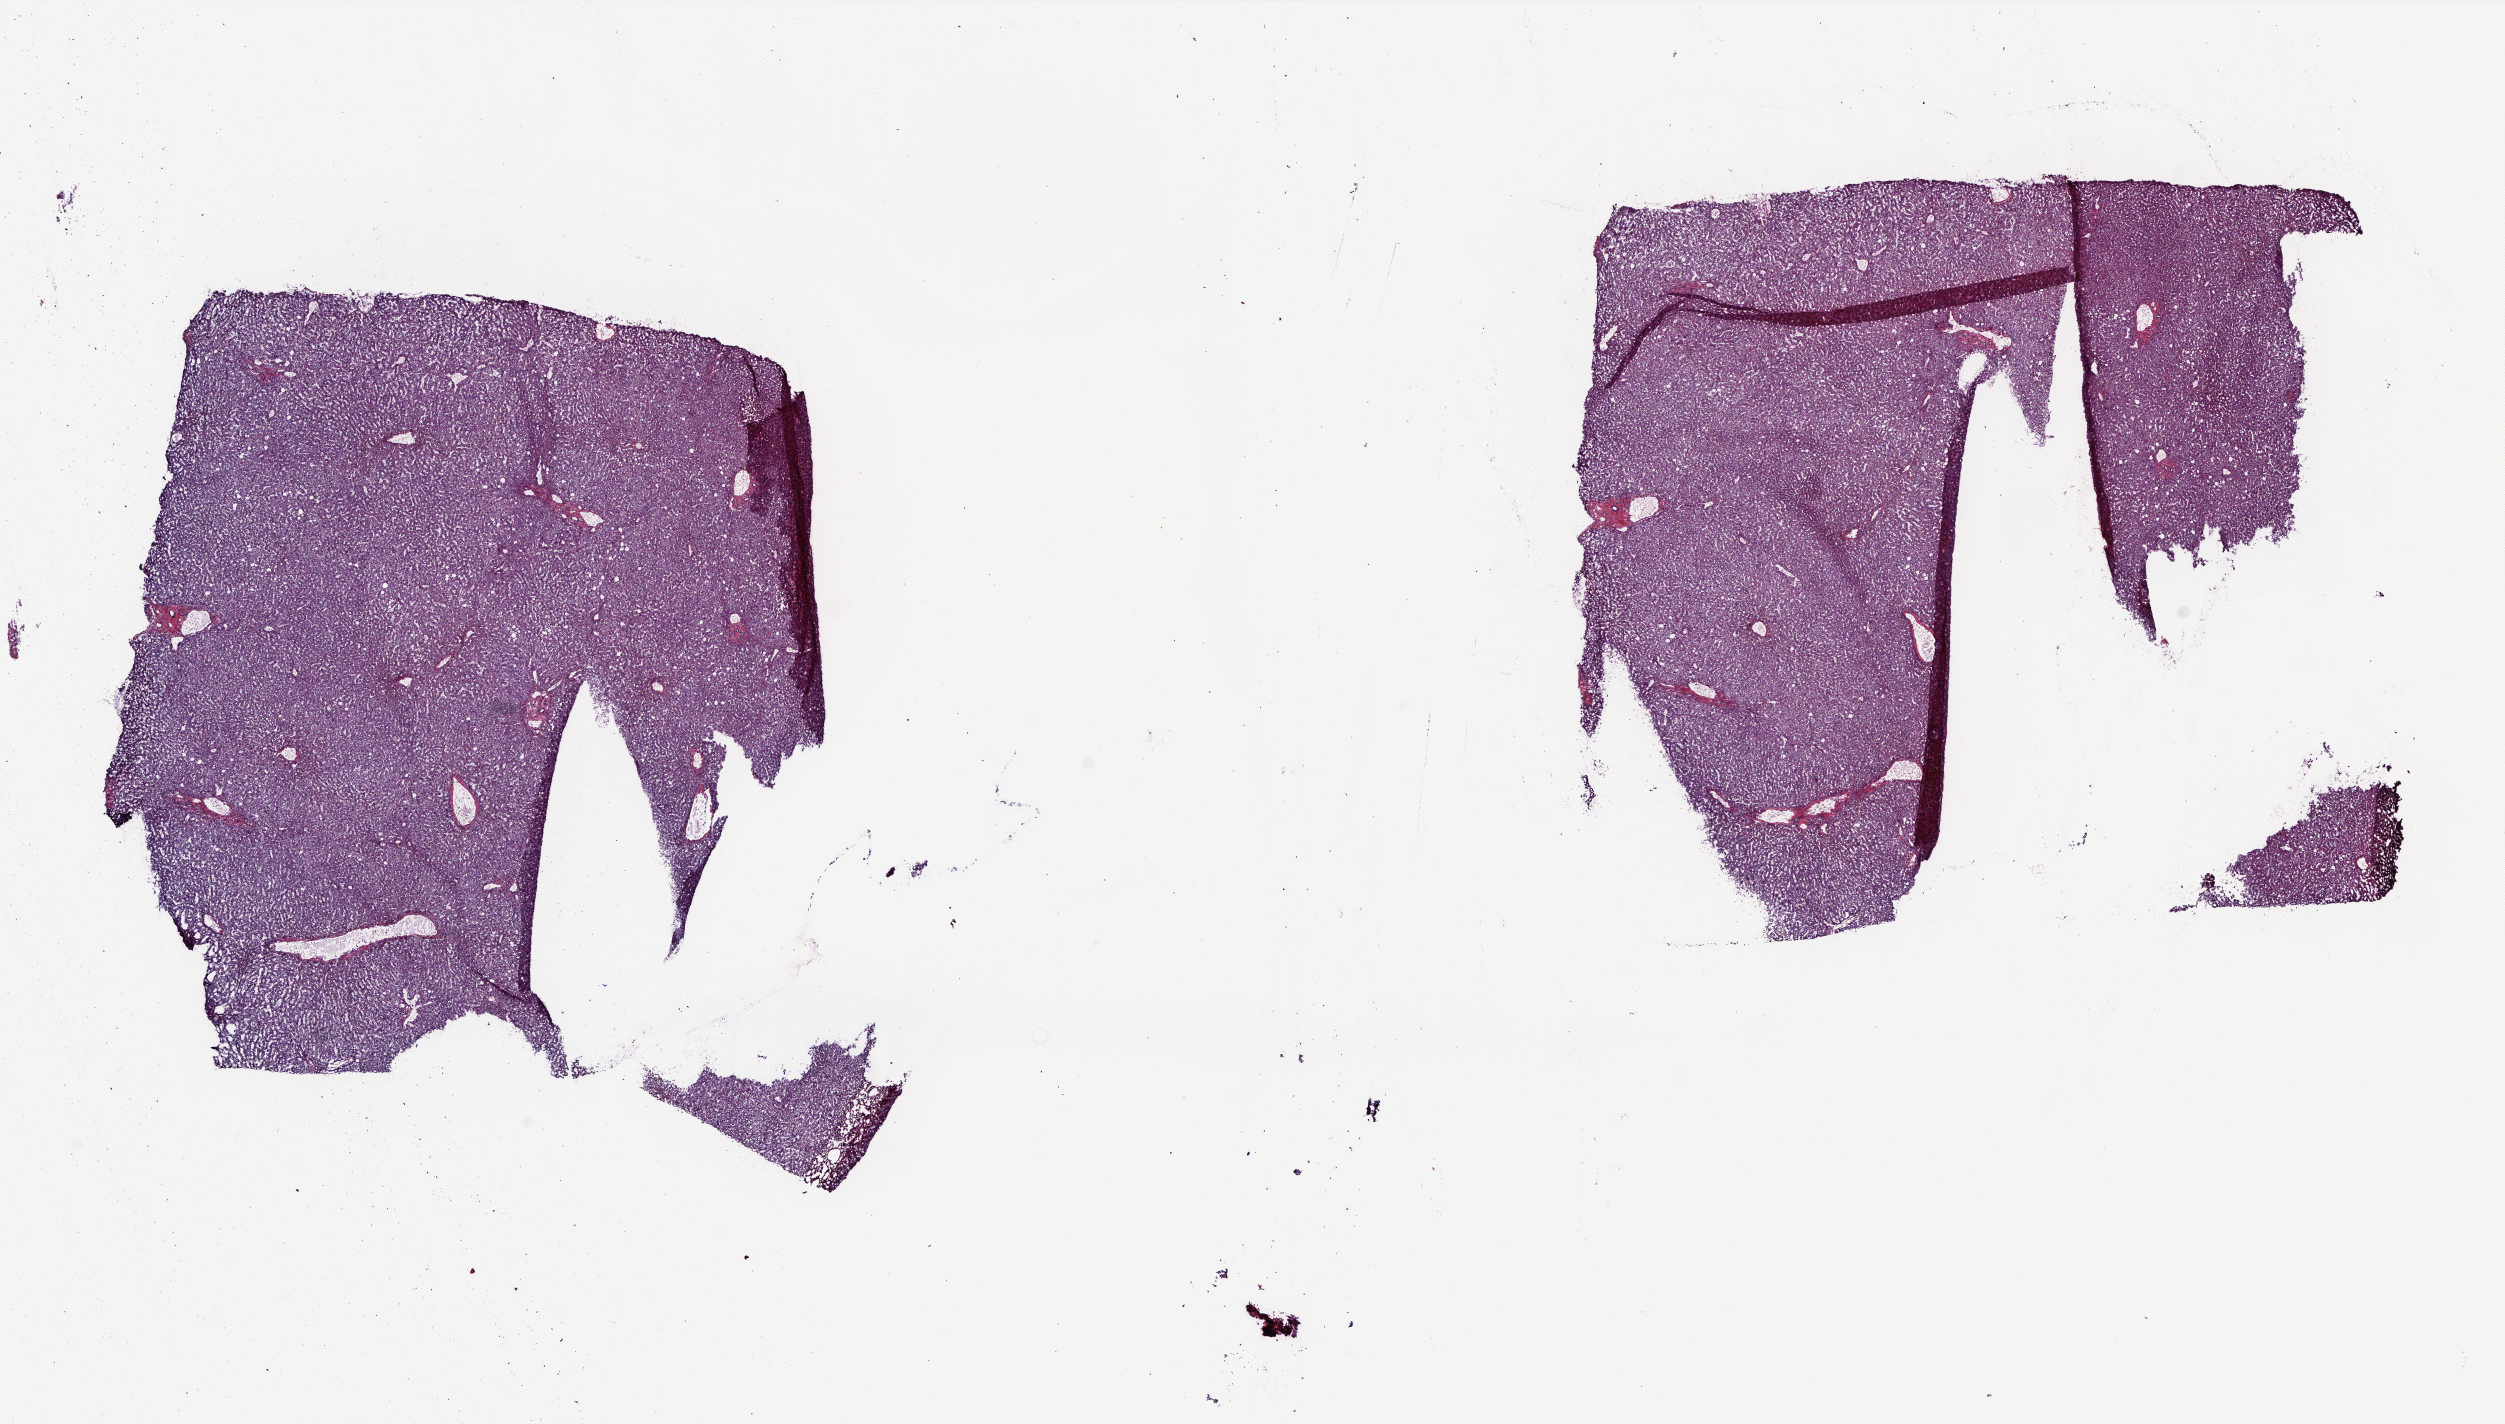
Hematoxylin and eosin (H&E) stained whole-slide image, whole scanned area (about 20.2 x 11.5 mm) shown as a low-resolution overview; frozen section; solid tissue normal (non-tumour tissue) sample from the liver. Female, age 75 years at initial diagnosis. Composition of this section per pathologist review: tumour cells 0%, tumour nuclei 0%, normal cells 100%, stromal cells 0%, necrosis 0%. Inflammatory infiltration, as recorded: lymphocyte infiltration 2%, monocyte infiltration 0%, neutrophil infiltration 0%.
* this section: solid tissue normal sample (biorepository sample class)
* patient diagnosis: Hepatocellular carcinoma, NOS